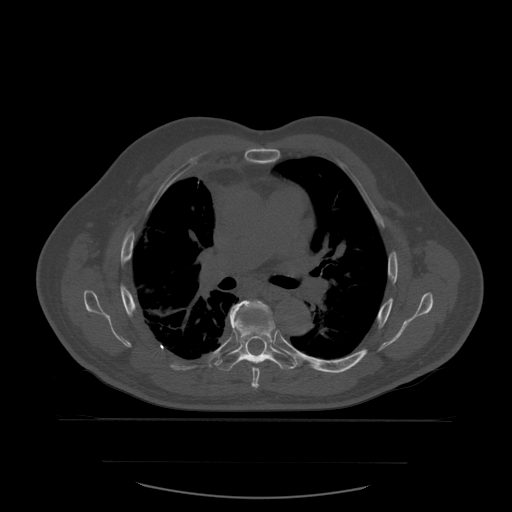
CT including the spine, one axial slice. Slice 392 of 590 in the series (ordered by position). Bone window (W 1800 / L 400 HU). 512 × 512 image matrix, field of view 479 × 479 mm. Patient age 71 years. From the clinical record (not read from this slice): primary cancer: lung; vertebrae with lytic lesions (as recorded): T1, T2, L5, S1.
Structures marked on this image (semi-automatic segmentation, software-assisted and operator-edited):
- T6 vertebra: bounding box [x1, y1, x2, y2] px = [238, 300, 269, 390]
- T7 vertebra: [217, 302, 298, 372]